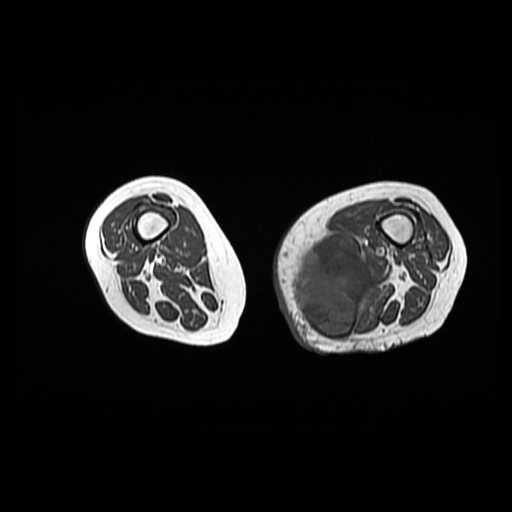
MRI of an extremity soft-tissue mass, one axial slice; slice 25 of 42 in the series (ordered by position); 6 mm slice thickness; 512 × 512 image matrix, field of view 420 × 420 mm. Female patient. Case-level facts recorded for this patient, not image findings: histological type: pleomorphic leiomyosarcoma; grade: high; site of the primary tumour: left thigh.
Outlined on this slice (manually delineated by an expert):
- gross tumour volume including surrounding oedema: bounding box <297,241,380,338> (left, top, right, bottom; pixels)
- gross tumour volume (mass): <297,241,373,338>